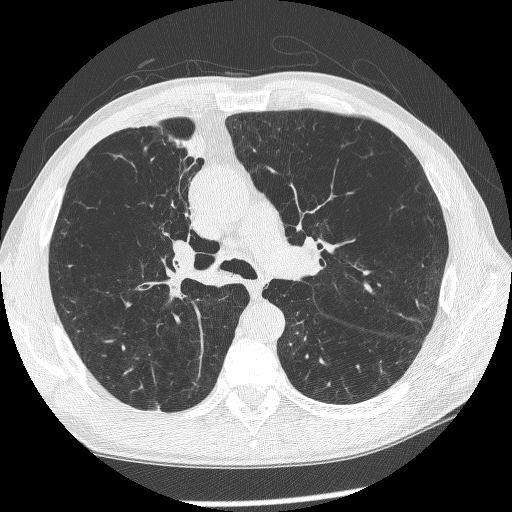
Low-dose screening chest CT, axial slice, baseline annual screen, lung window (W 1500 / L -600 HU), slice 157 of 266 in the series. Male, age 60 years at enrolment. Current smoker at enrolment.
Expert-annotated lung lesion, bounding box [x1, y1, x2, y2] px = [144, 207, 225, 299]. Screening reader's record for this exam (one nodule recorded; not confirmed to be the boxed lesion): non-calcified nodule or mass ≥4 mm, right upper lobe, 12 × 8 mm, spiculated (stellate) margins, mixed attenuation. Later outcome: lung cancer diagnosed 208 days after this screen — squamous cell carcinoma, NOS, right upper lobe, right middle lobe, right main stem bronchus, poorly differentiated (G3), stage IV (AJCC 6th edition).